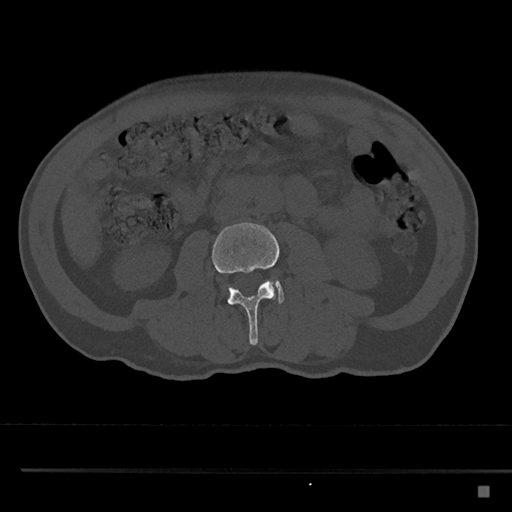
CT including the spine, one axial slice; position 686 of 797 along the scan axis; reconstruction kernel Br40s/3; bone window (W 1800 / L 400 HU); 0.5 mm slice thickness; 512 × 512 image matrix, field of view 391 × 391 mm. Patient: male, 59 years. Case-level facts recorded for this patient, not image findings: primary cancer: prostate.
Structures marked on this image (semi-automatic segmentation, software-assisted and operator-edited):
- L3 vertebra: box from (x=212, y=222) to (x=280, y=345) px
- L4 vertebra: (x=224, y=279)–(x=285, y=304)